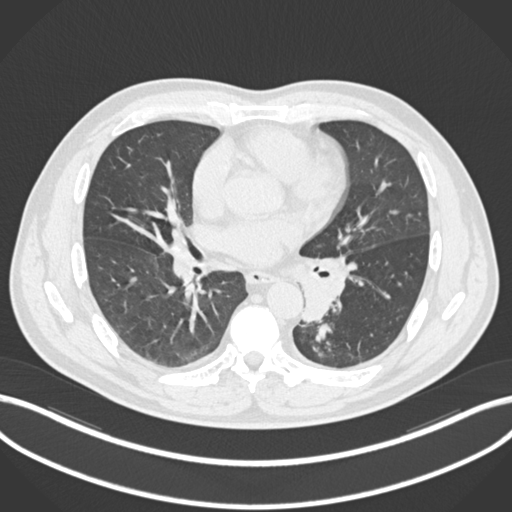
Chest CT, one axial slice. Lung window (W 1500 / L -600 HU). 512 × 512 image matrix, field of view 400 × 400 mm. Patient: male, 50 years. Case-level facts recorded for this patient, not image findings: clinical TNM (as recorded): T2a N3 M0.
Structures marked on this image (bounding box drawn by a radiologist):
- lung tumour (recorded histology: squamous cell carcinoma): bounding box <294,264,350,327> (left, top, right, bottom; pixels)